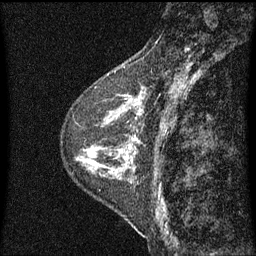
Breast MRI (dynamic contrast-enhanced), one sagittal slice. Dynamic contrast-enhanced series, image 2 of 3 at this slice position (ordered by acquisition). 1.5 T. TE 4.2 ms, TR 8 ms. 2 mm slice thickness. 256 × 256 image matrix. Patient: female, 48 years.
Structures marked on this image (semi-automatic segmentation, software-assisted and operator-edited):
- analysis volume of interest (the breast-tissue region the enhancement analysis was run in; not a lesion): box from (x=103, y=74) to (x=145, y=139) px
- tumour enhancement mask (voxels above the 70 % enhancement threshold inside the analysis volume of interest): (x=104, y=90)–(x=145, y=139)